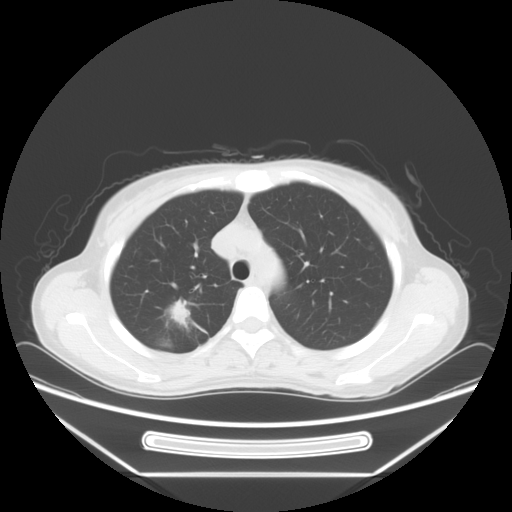
Chest CT, one axial slice; slice 50 of 66 in the series (ordered by position); reconstruction kernel STANDARD; 120 kVp; lung window (W 1500 / L -600 HU); 512 × 512 image matrix. Female patient, age 37 years. From the clinical record (not read from this slice): clinical TNM (as recorded): T1c N0 M1.
Annotated regions visible in this slice (bounding box drawn by a radiologist):
- lung tumour (recorded histology: adenocarcinoma): box from (x=168, y=292) to (x=192, y=331) px